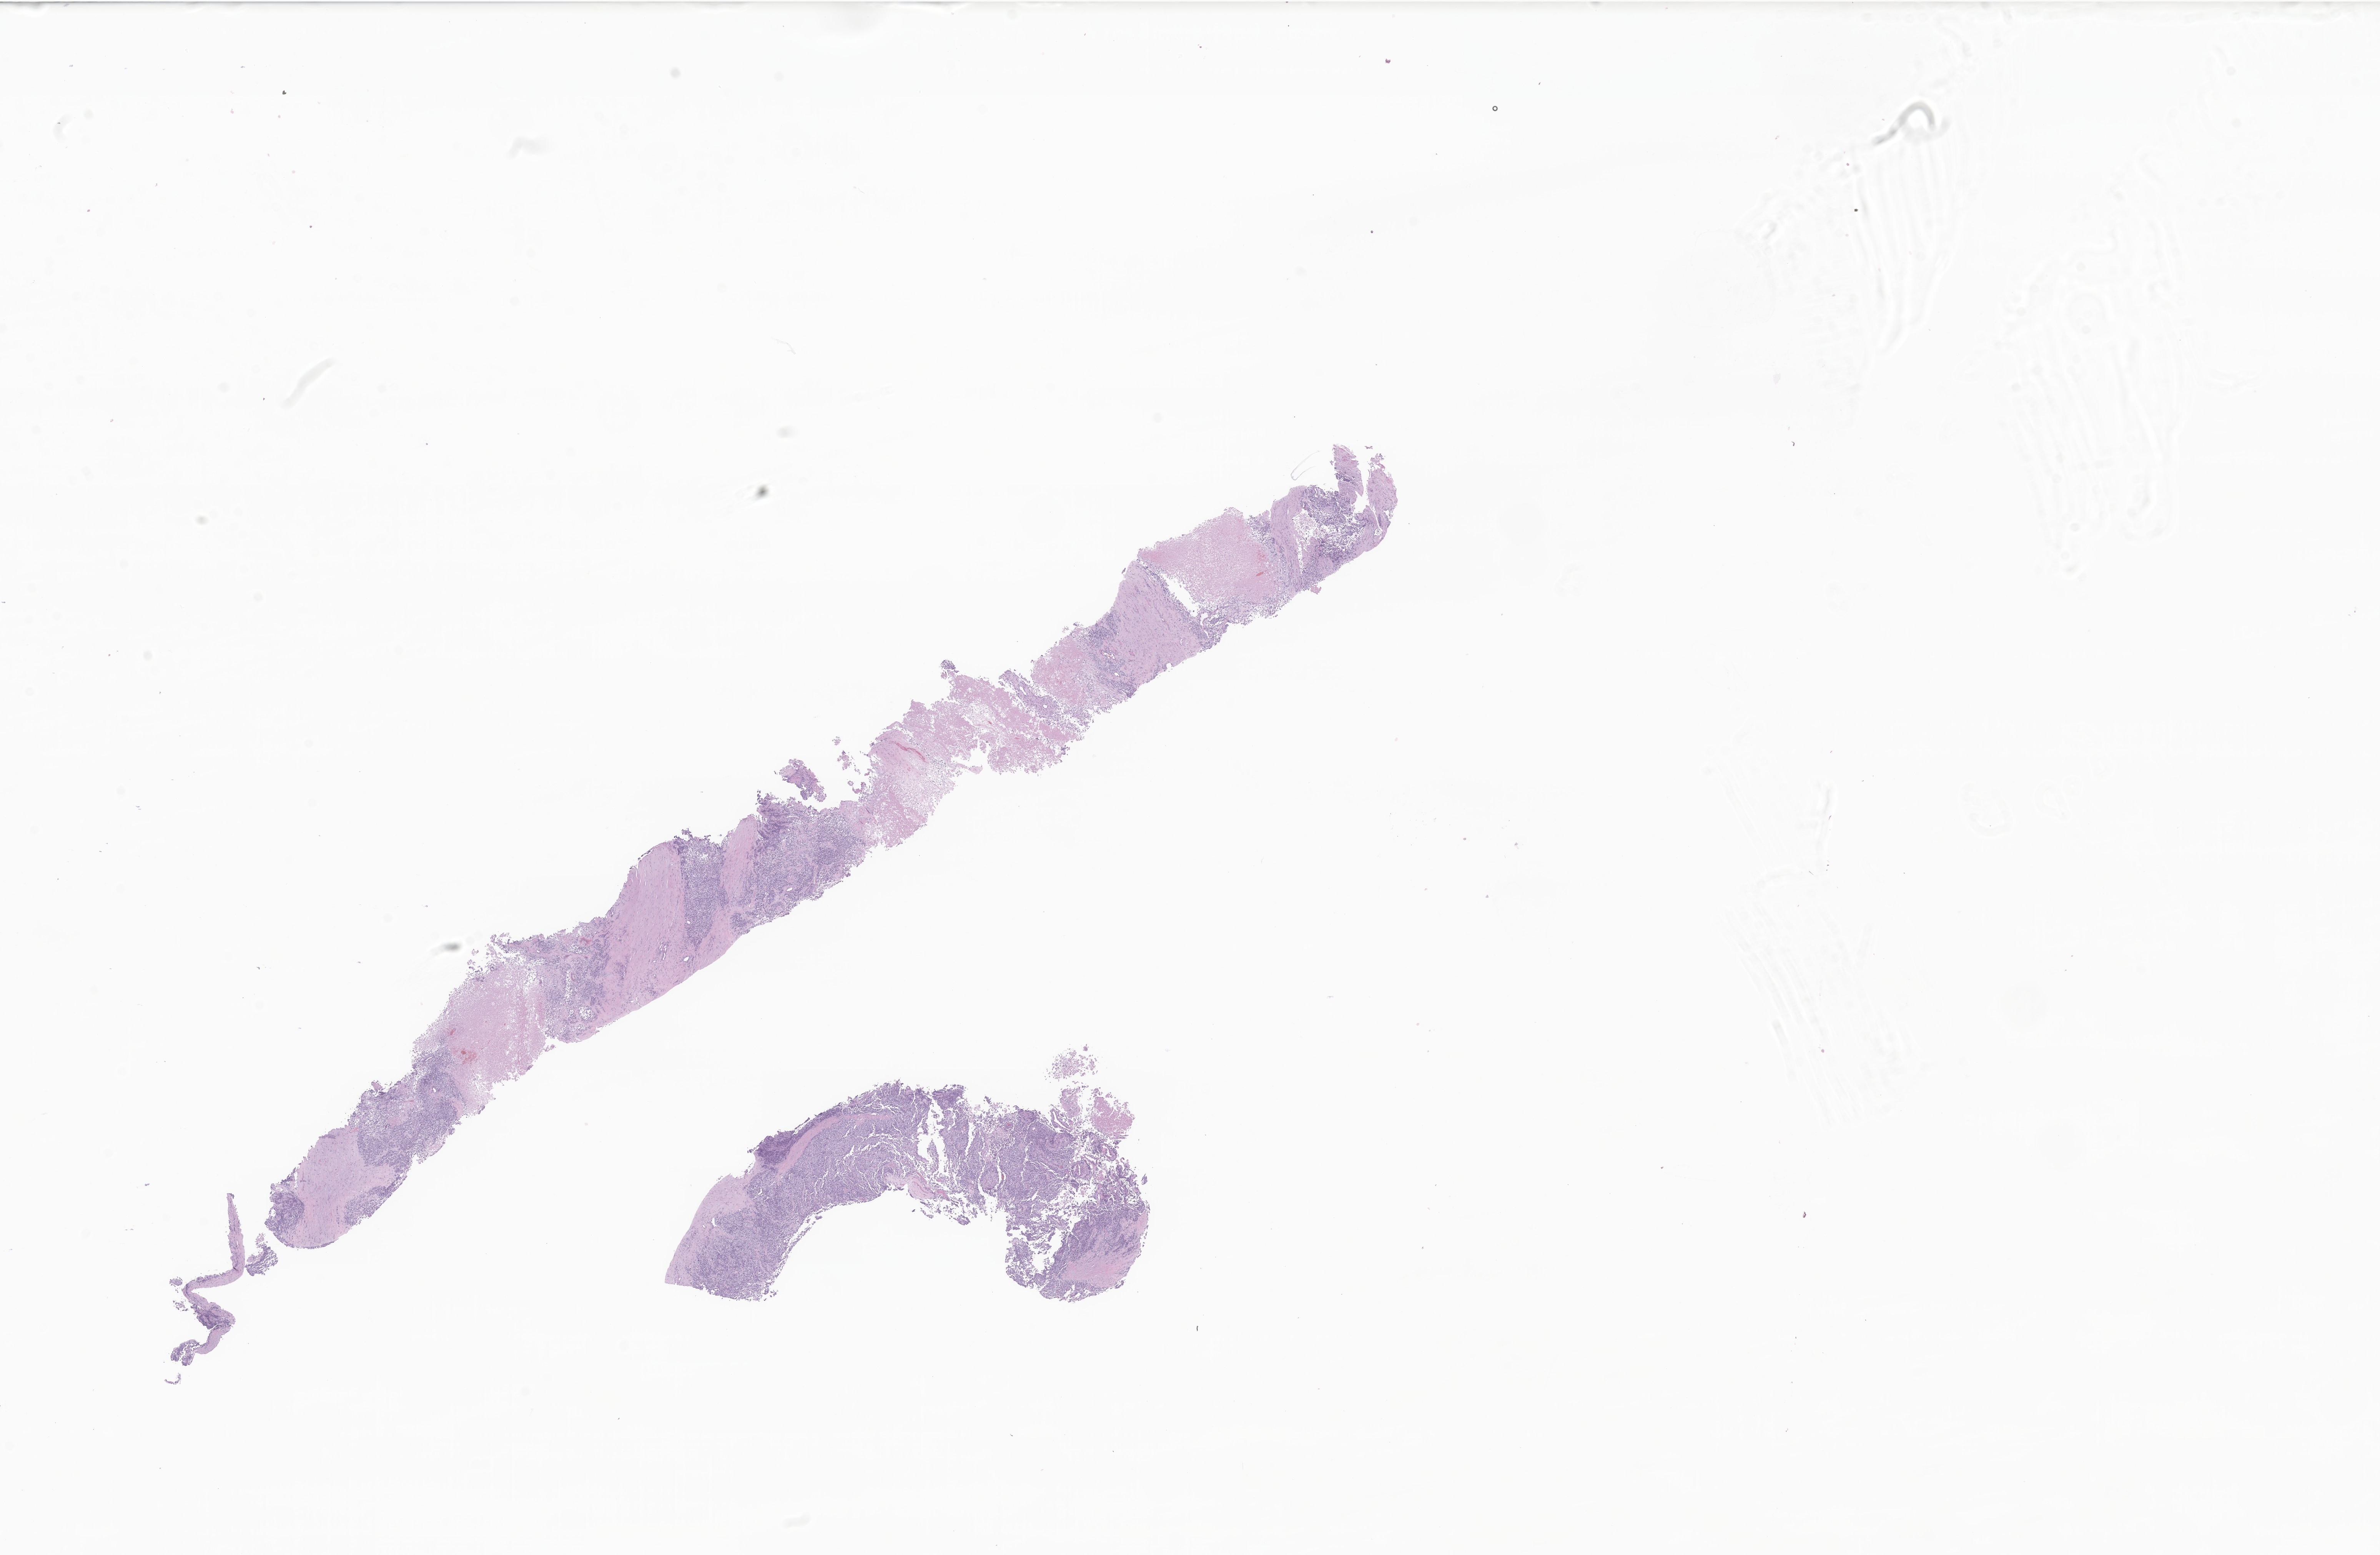
Whole-slide image, hematoxylin and eosin (H&E) stain of tumor tissue from the soft tissue of upper extremity — whole scanned area (about 26.1 x 17.0 mm) shown as a low-resolution overview, FFPE section. Patient: female, age 212 months (17 years 8 months).
Recorded diagnosis: Alveolar rhabdomyosarcoma. Tissue or organ of origin (case record): connective, subcutaneous and other soft tissues of upper limb and shoulder.